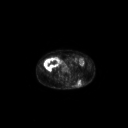
FDG PET of an extremity soft-tissue mass (from a PET/CT study), one axial slice. 3.27 mm slice thickness. 128 × 128 image matrix. Male patient, age 69 years. Case-level facts recorded for this patient, not image findings: histological type: leiomyosarcoma; grade: intermediate; site of the primary tumour: left pelvis.
Outlined on this slice (expert contour drawn on MRI and transferred to this co-registered scan by the dataset authors):
- gross tumour volume (mass): box from (x=76, y=79) to (x=83, y=86) px